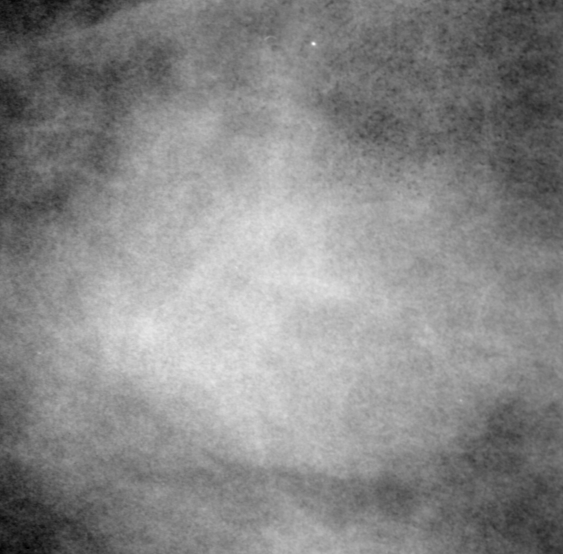
Cropped region of a digitized screen-film mammogram centred on a radiologist-marked abnormality; right breast; CC view.
Finding: mass, shape oval, margins obscured; BI-RADS assessment category 0 (incomplete: needs additional imaging); subtlety rating 4 on a 1 (subtle) to 5 (obvious) scale; pathology (as recorded): benign.